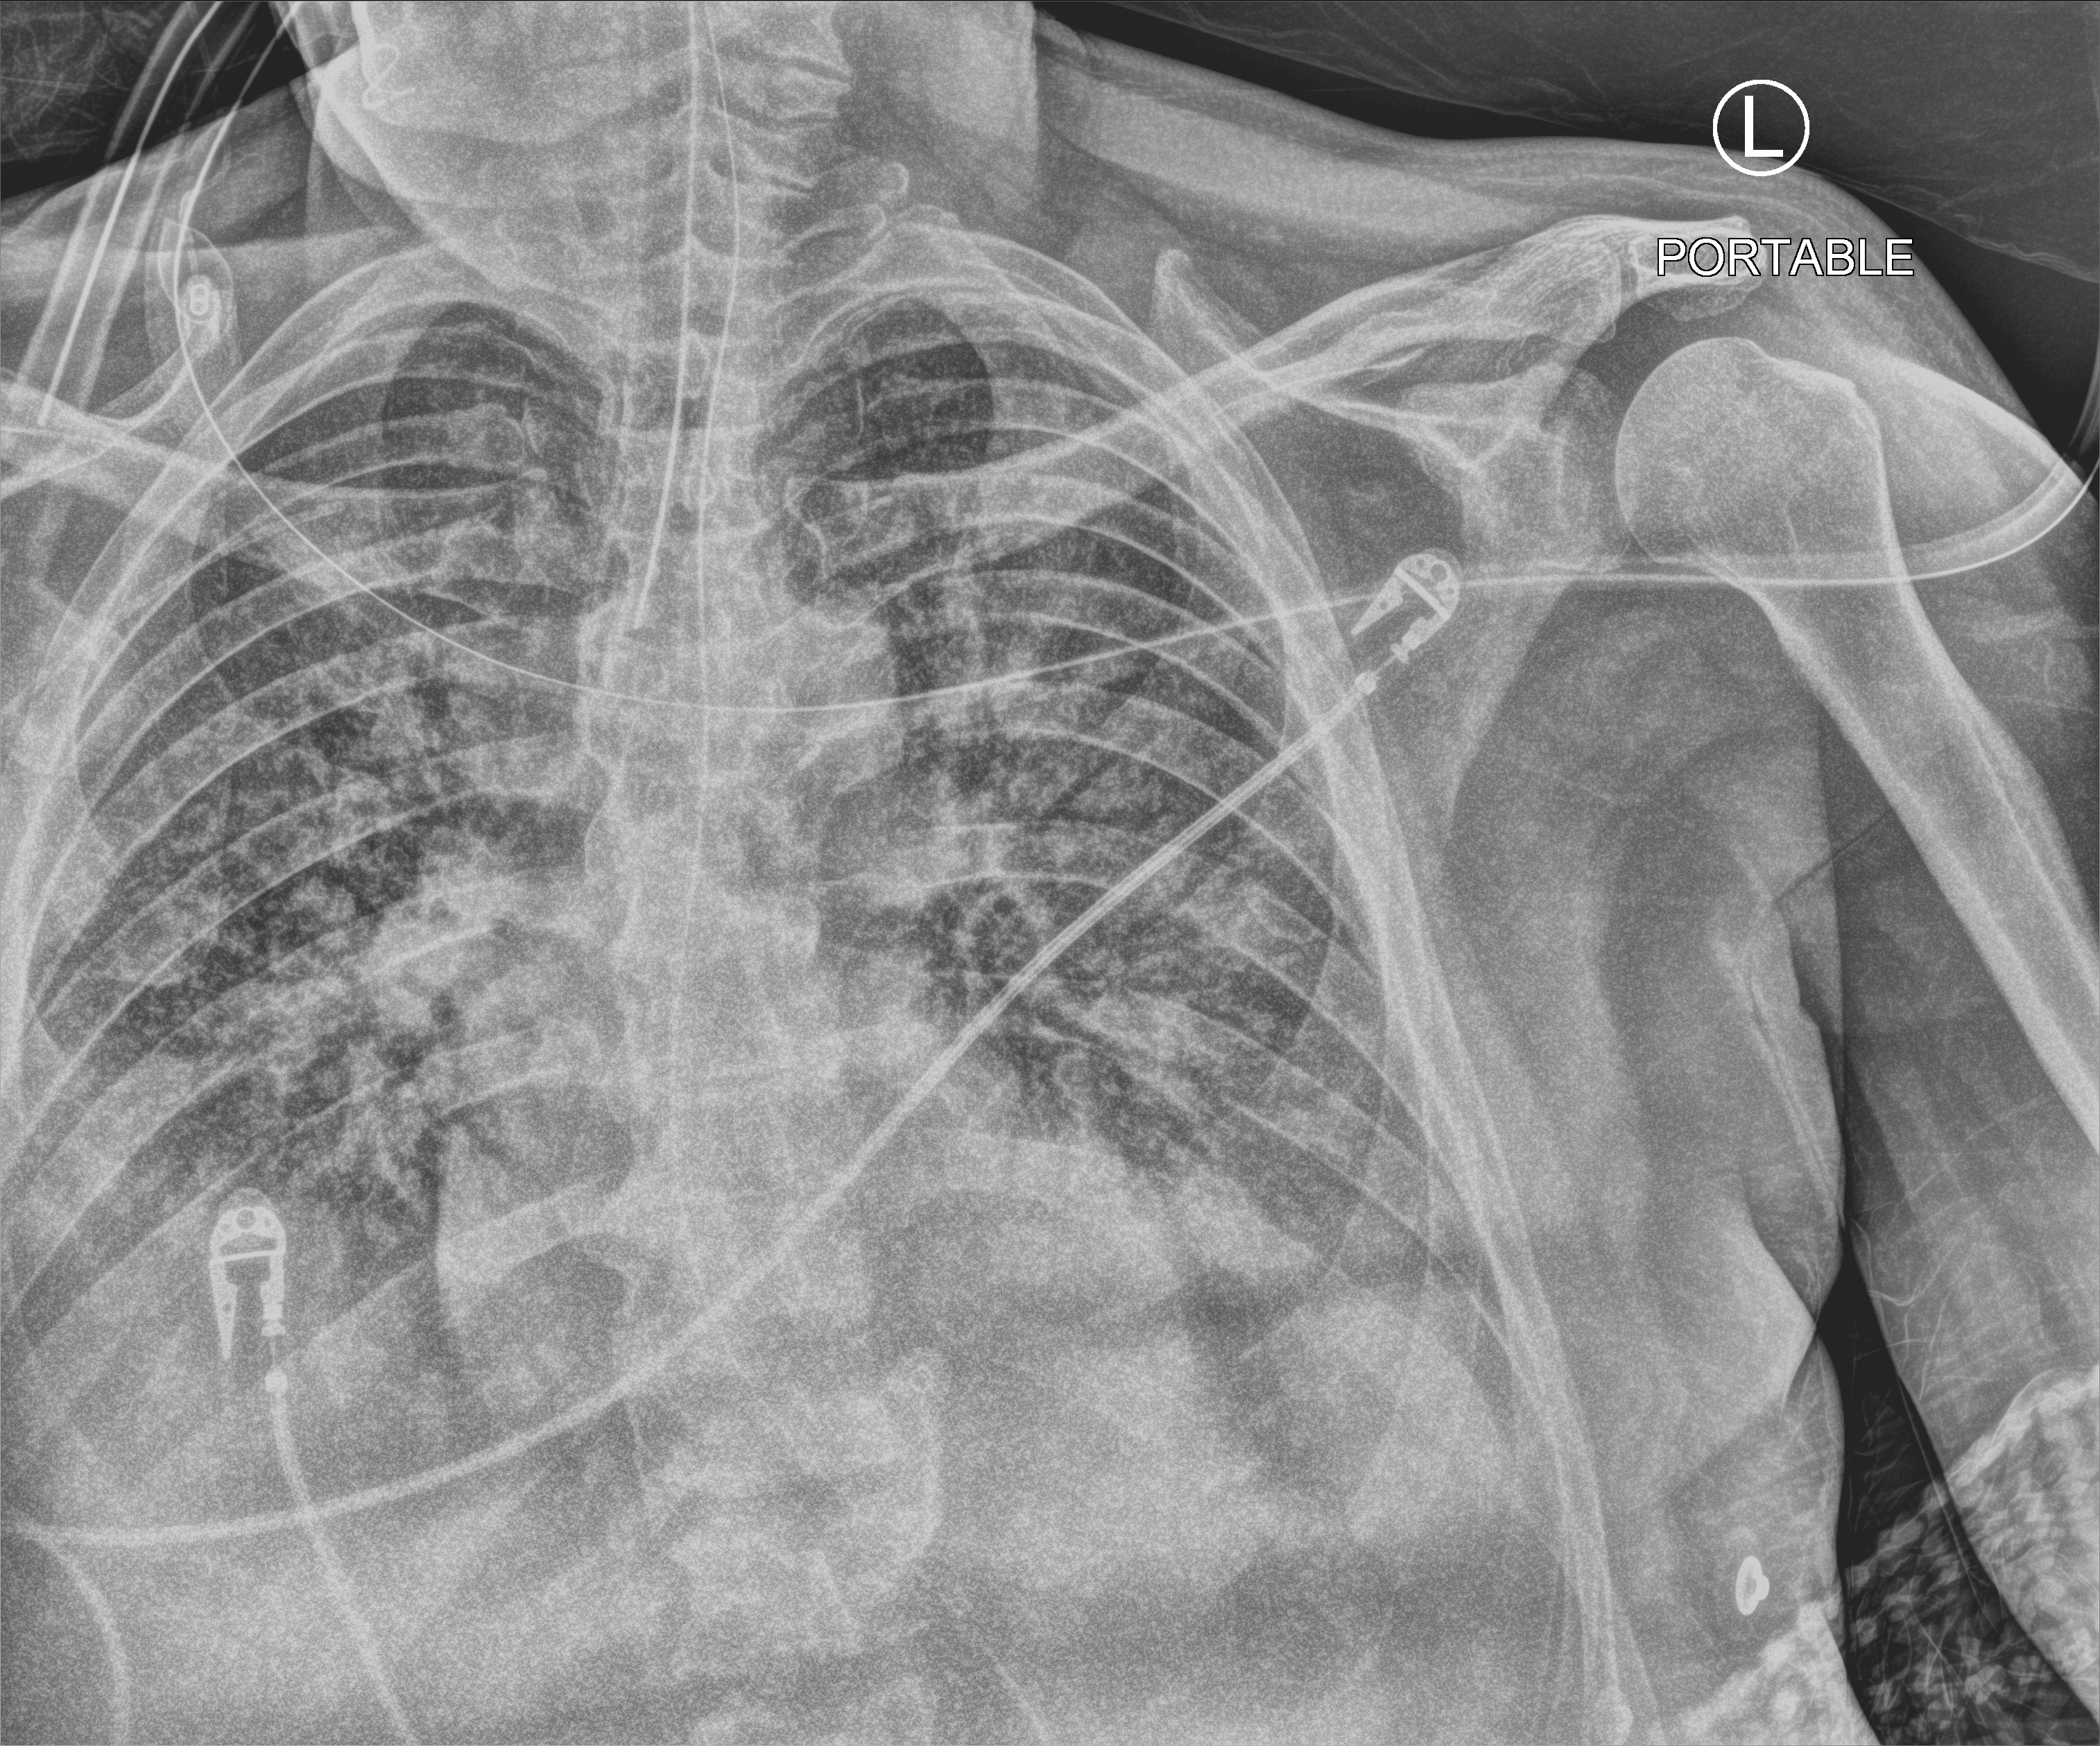
Portable chest radiograph, anteroposterior (AP) projection. Male patient hospitalised with COVID-19, age 60–74 years.
From the hospital-stay record, not from the radiograph (when in the stay this image was taken is not recorded):
- COPD (admission record): no